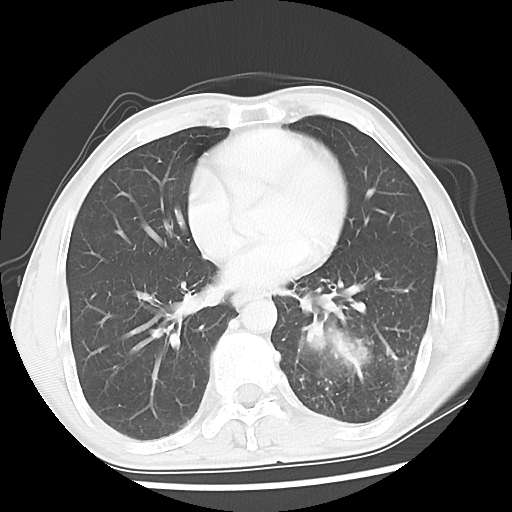
Chest CT, one axial slice. 120 kVp. Lung window (W 1500 / L -600 HU). 5 mm slice thickness. 512 × 512 image matrix. Male patient, age 60 years. Case-level facts recorded for this patient, not image findings: clinical TNM (as recorded): T4 N0 M0.
Annotated regions visible in this slice (rectangle marked by the reading radiologist):
- lung tumour (recorded histology: squamous cell carcinoma): bounding box [x1, y1, x2, y2] px = [298, 305, 385, 380]